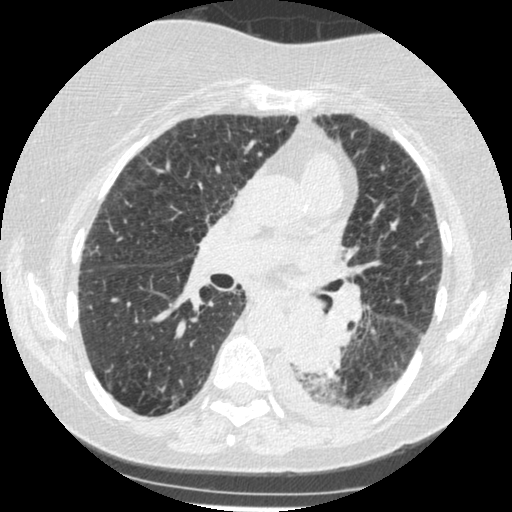
Low-dose screening chest CT, one axial slice. Slice 138 of 341 in the series (ordered by position). Reconstruction kernel STANDARD. 120 kVp. Lung window (W 1500 / L -600 HU). 512 × 512 image matrix, field of view 310 × 310 mm.
Annotated regions visible in this slice (outlined manually by an expert reader):
- lesion 1 (tumor, lower lobe of left lung): bounding box <285,309,340,374> (left, top, right, bottom; pixels)